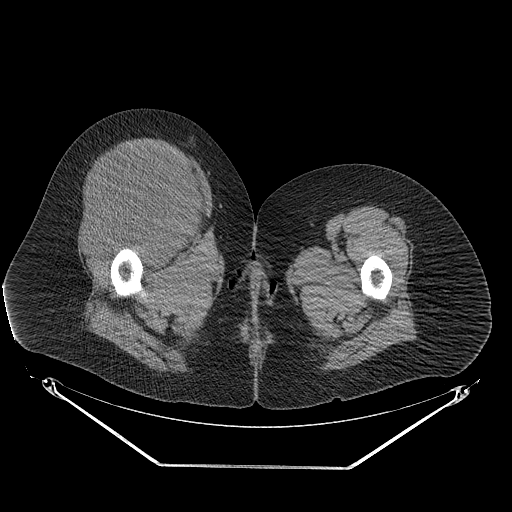
CT of an extremity soft-tissue mass (from a PET/CT study), one axial slice; position 47 of 267 along the scan axis; 140 kVp; soft-tissue window (W 400 / L 40 HU); 3.75 mm slice thickness; 512 × 512 image matrix, field of view 500 × 500 mm. Female patient. Case-level facts recorded for this patient, not image findings: histological type: malignant solitary fibrous tumor; grade: intermediate; site of the primary tumour: right thigh.
Structures marked on this image (expert contour drawn on MRI and transferred to this co-registered scan by the dataset authors):
- gross tumour volume including surrounding oedema: bounding box [x1, y1, x2, y2] px = [77, 146, 206, 245]
- gross tumour volume (mass): [82, 146, 202, 241]